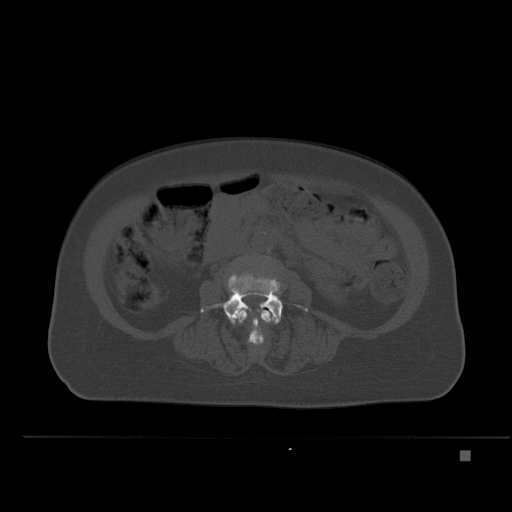
CT including the spine, one axial slice; slice 185 of 477 in the series (ordered by position); bone window (W 1800 / L 400 HU); 512 × 512 image matrix, field of view 422 × 422 mm. Female patient, age 74 years. From the clinical record (not read from this slice): primary cancer: colon.
Outlined on this slice (semi-automatically segmented with operator editing):
- L3 vertebra: bounding box [x1, y1, x2, y2] px = [237, 306, 274, 346]
- L4 vertebra: [200, 273, 307, 342]